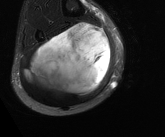
MRI of an extremity soft-tissue mass, one axial slice; slice 69 of 81 in the series (ordered by position); T2-weighted fat-saturated; MR volume resampled by the dataset authors to the PET/CT grid (not the native acquisition matrix); 3.27 mm slice thickness; 165 × 137 image matrix, field of view 161 × 134 mm. Male patient. Case-level facts recorded for this patient, not image findings: histological type: liposarcoma - round cell; grade: high; site of the primary tumour: right calf.
Annotated regions visible in this slice (expert contour drawn on MRI and transferred to this co-registered scan by the dataset authors):
- gross tumour volume (mass): box from (x=25, y=23) to (x=111, y=97) px